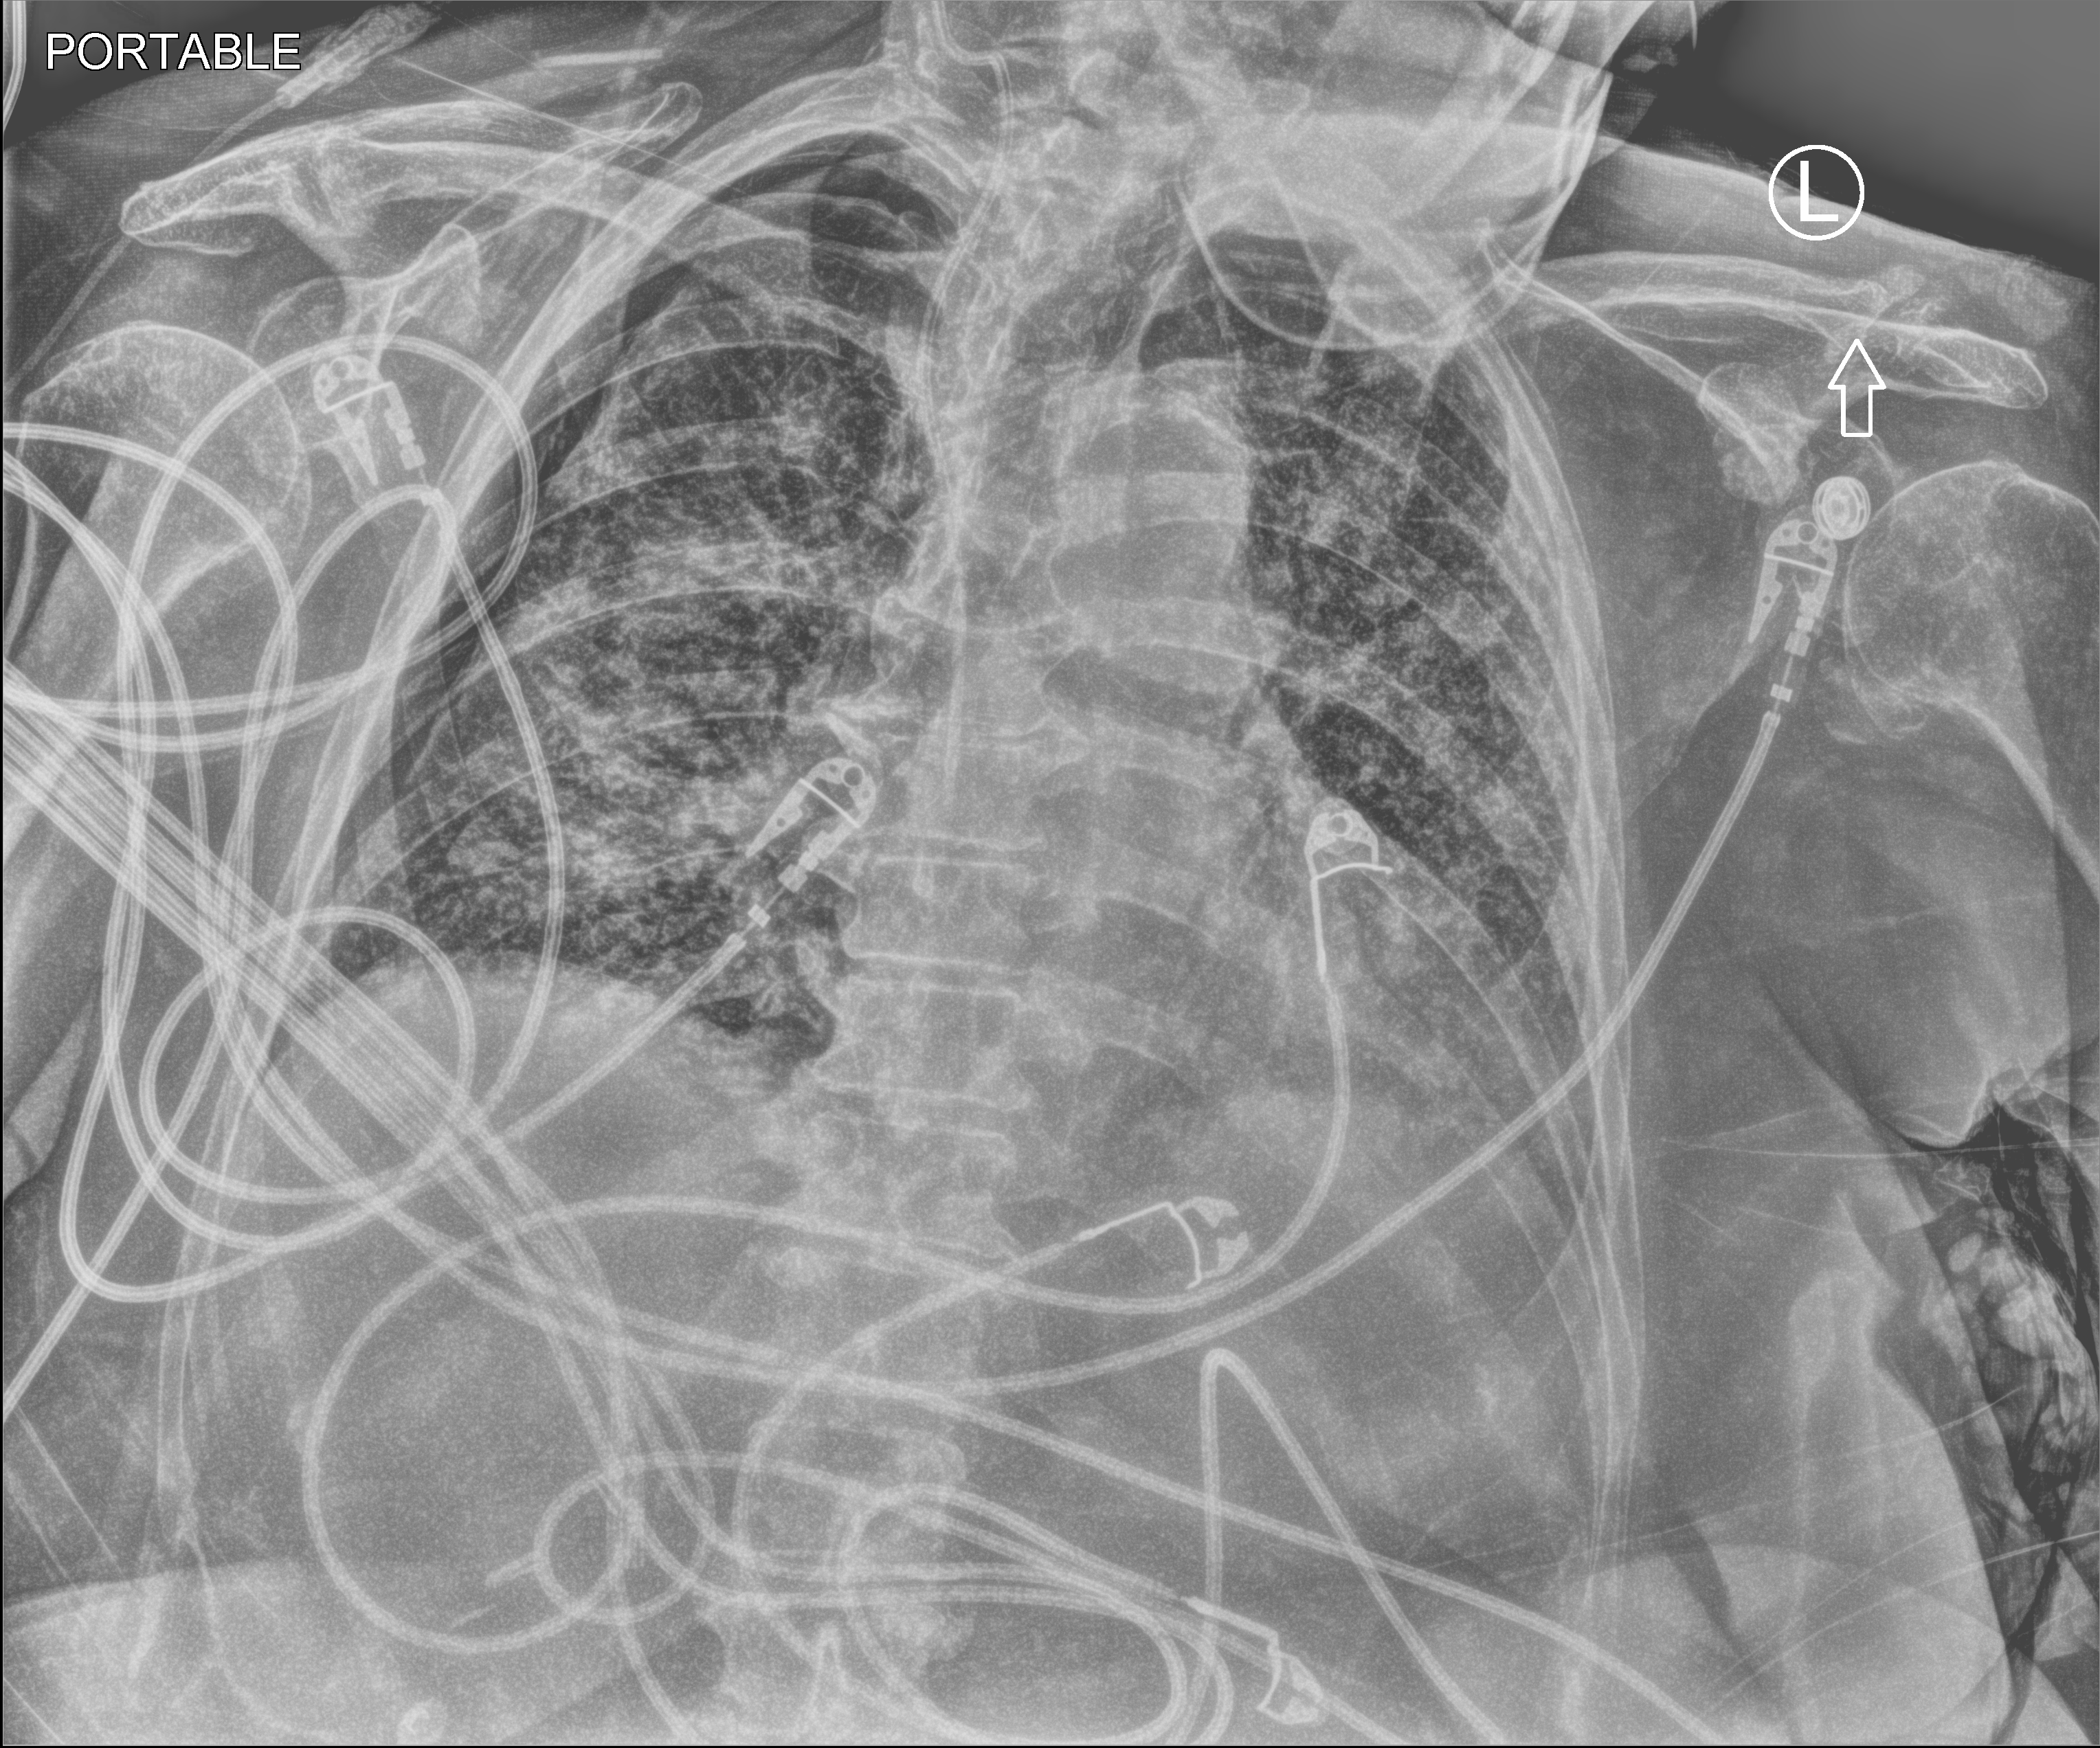
Chest X-ray (portable), anteroposterior (AP) projection. Patient hospitalised with COVID-19; female, aged 75–90 years.
Admission-level facts for this patient (not findings on this image; timing relative to this image not recorded): admitted to intensive care during this hospital stay: no; smoking status (admission record): former.